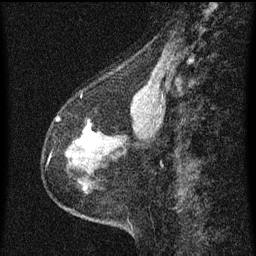
Breast MRI (dynamic contrast-enhanced), one sagittal slice; slice 24 of 60 in the series (ordered by position); dynamic contrast-enhanced series, image 2 of 3 at this slice position (ordered by acquisition); 1.5 T; TE 4.2 ms, TR 8 ms; 2 mm slice thickness; 256 × 256 image matrix, field of view 180 × 180 mm. Patient: female, 56 years.
Annotated regions visible in this slice (semi-automatically segmented with operator editing):
- analysis volume of interest (the breast-tissue region the enhancement analysis was run in; not a lesion): box from (x=52, y=118) to (x=102, y=181) px
- tumour enhancement mask (voxels above the 70 % enhancement threshold inside the analysis volume of interest): (x=73, y=129)–(x=91, y=156)